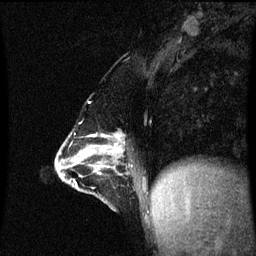
Breast MRI (dynamic contrast-enhanced), one sagittal slice; position 25 of 60 along the scan axis; dynamic contrast-enhanced series, image 2 of 3 at this slice position (ordered by acquisition); 1.5 T; TE 4.2 ms, TR 8.9 ms; 2 mm slice thickness; 256 × 256 image matrix, field of view 200 × 200 mm. Patient: female, 47 years. Case-level facts recorded for this patient, not image findings: setting: breast cancer imaged before/during neoadjuvant chemotherapy; receptor status: HR-positive, HER2-negative.
Outlined on this slice (semi-automatically segmented with operator editing):
- analysis volume of interest (the breast-tissue region the enhancement analysis was run in; not a lesion): box from (x=57, y=132) to (x=148, y=209) px
- tumour enhancement mask (voxels above the 70 % enhancement threshold inside the analysis volume of interest): (x=79, y=134)–(x=124, y=155)